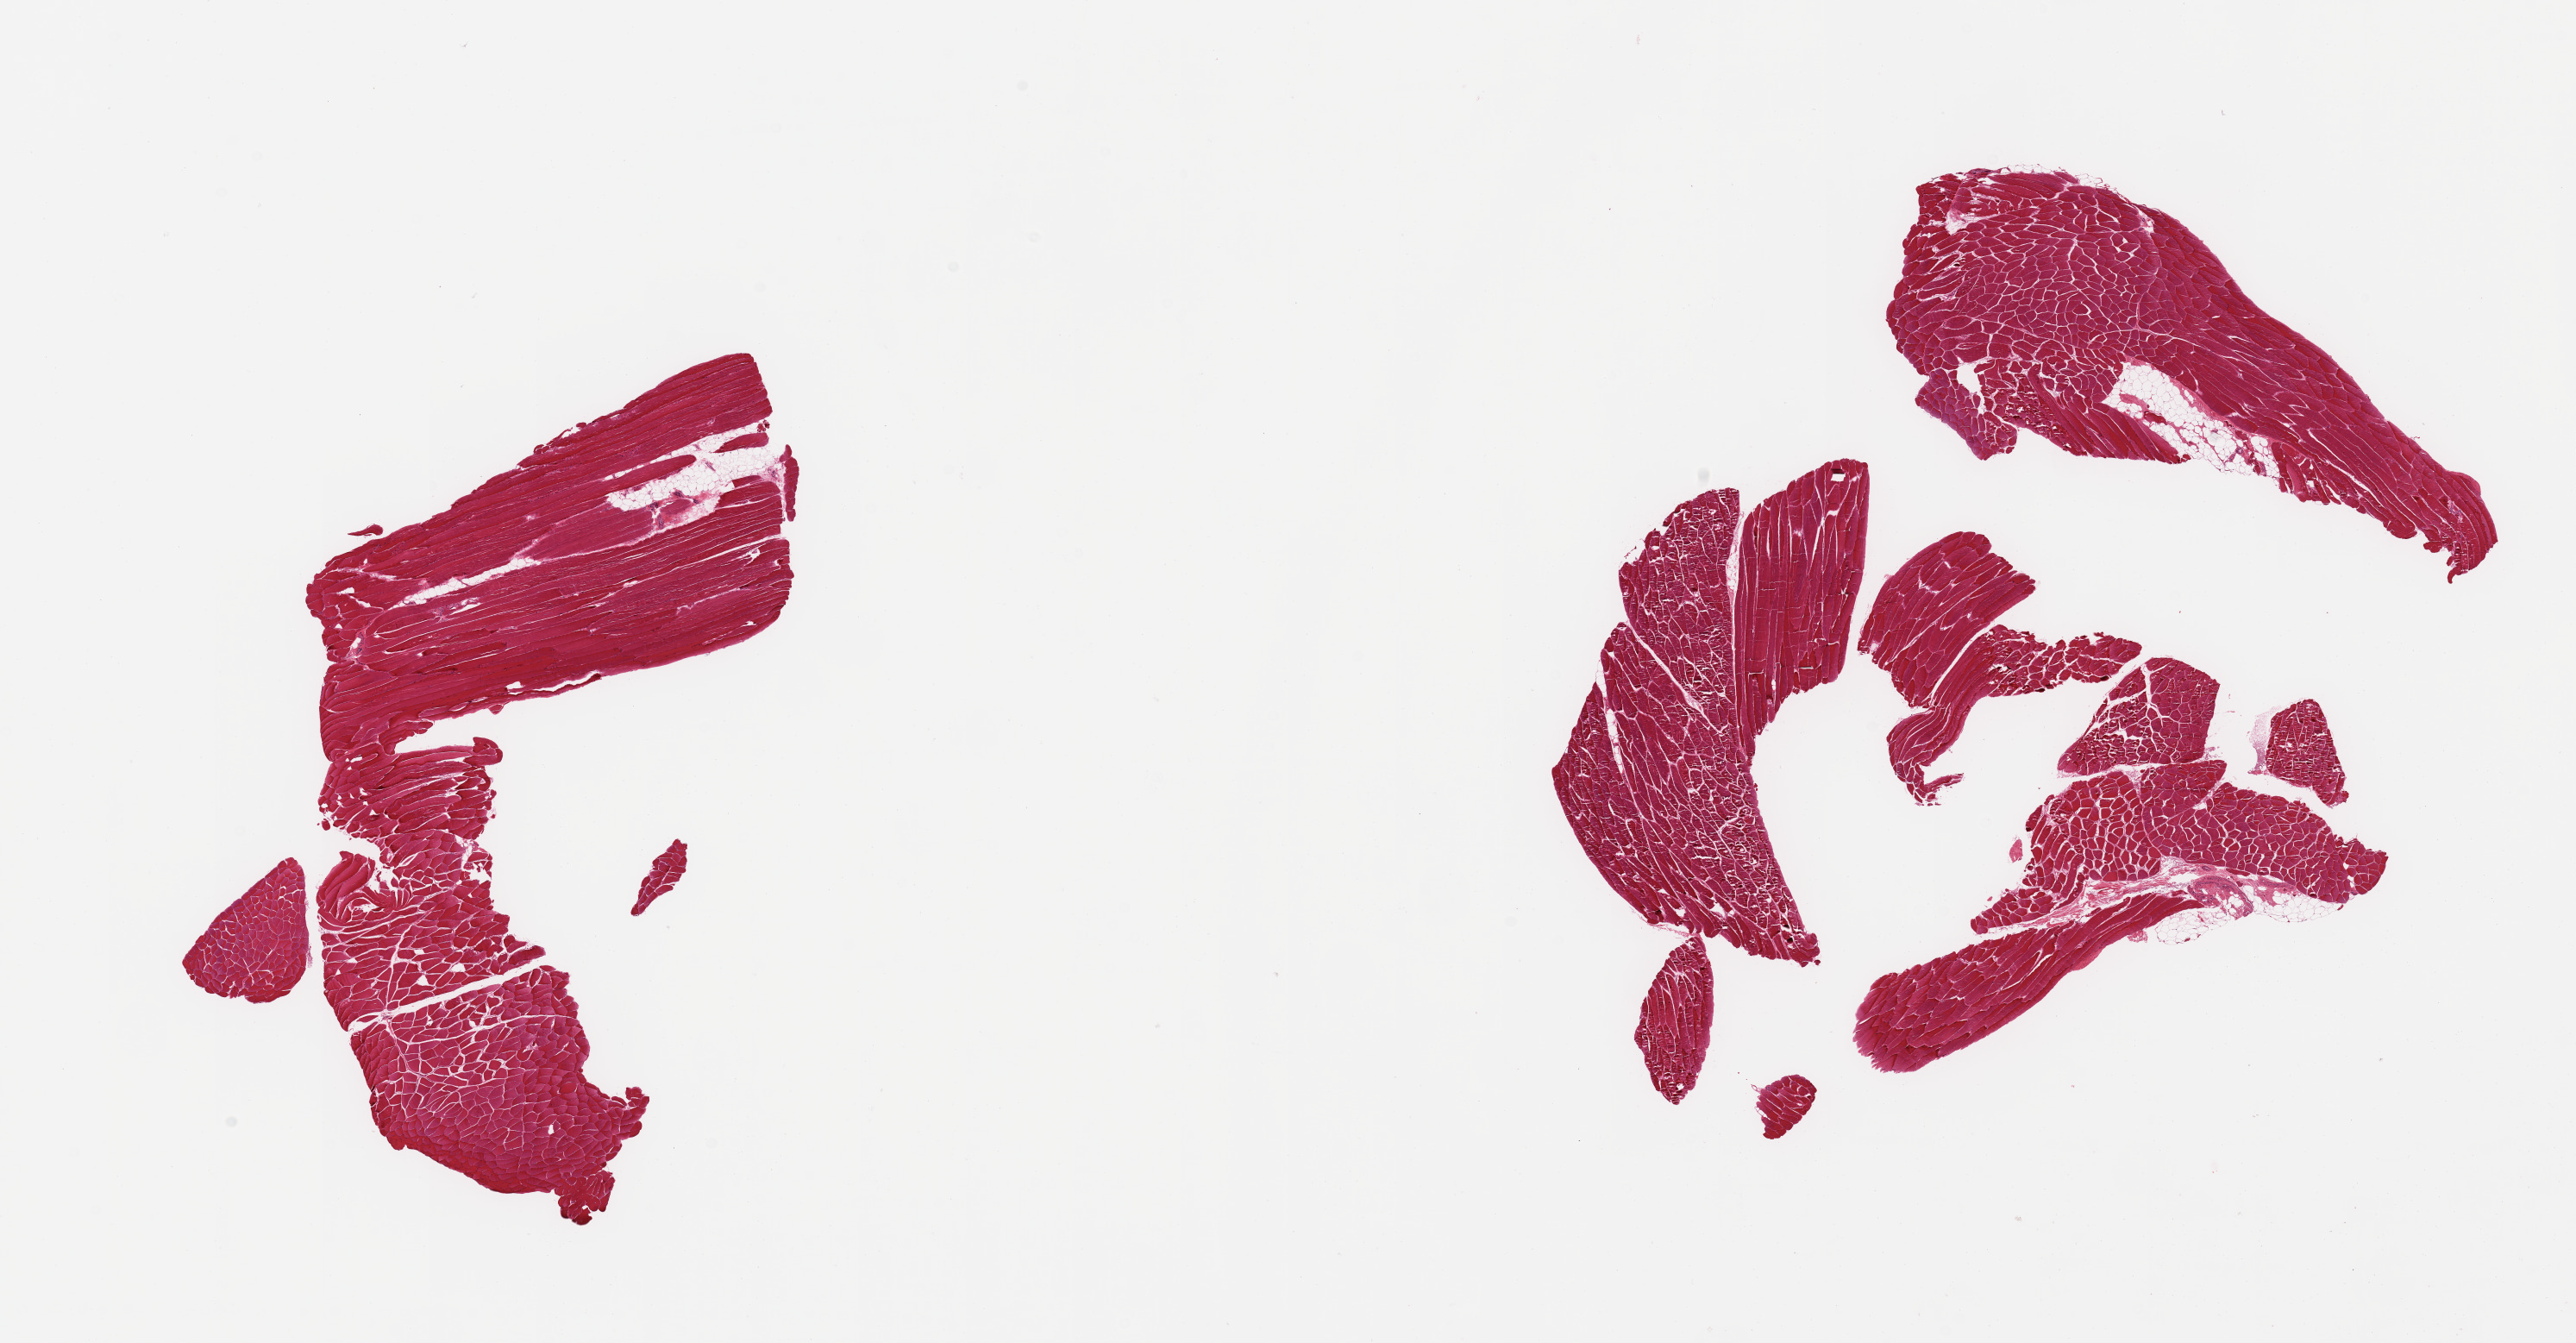
Digitized haematoxylin and eosin-stained section — low-resolution overview of the scanned area, about 23.6 x 12.3 mm; PAXgene-fixed paraffin-embedded (PFPE) section; target tissue: skeletal muscle; donor tissue sample. Donor sex: male.
Pathologist's review note for this sample: 2 pieces (fragmented); includes <10% fat.